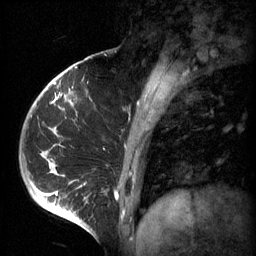
Breast MRI (dynamic contrast-enhanced), one sagittal slice; slice 19 of 60 in the series (ordered by position); 3 images stored at this slice position (order not interpretable as contrast timing); 1.5 T; TE 4.2 ms, TR 11 ms; 2 mm slice thickness; 256 × 256 image matrix, field of view 200 × 200 mm. Female patient, age 51 years.
Outlined on this slice (semi-automatic segmentation, software-assisted and operator-edited):
- analysis volume of interest (the breast-tissue region the enhancement analysis was run in; not a lesion): bounding box <48,82,161,197> (left, top, right, bottom; pixels)
- tumour enhancement mask (voxels above the 70 % enhancement threshold inside the analysis volume of interest): <48,82,159,197>